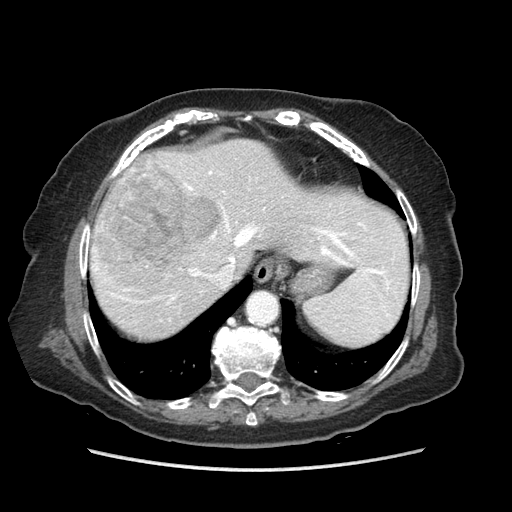
Contrast-enhanced abdominal CT (liver protocol), one axial slice; slice 67 of 89 in the series (ordered by position); soft-tissue window (W 400 / L 40 HU); 512 × 512 image matrix, field of view 360 × 360 mm. From the clinical record (not read from this slice): diagnosis: hepatocellular carcinoma (patient treated with transarterial chemoembolisation; whether this scan precedes or follows treatment is not stated here); TNM stage (as recorded): Stage-IIIA; Child-Pugh class: A; tumour nodularity: multinodular.
Outlined on this slice (semi-automatic segmentation, software-assisted and operator-edited):
- abdominal aorta: box from (x=248, y=293) to (x=277, y=324) px
- liver parenchyma outside the tumour (the mass and vessels are separate outlines, so this box may not span the whole liver): (x=90, y=138)–(x=406, y=338)
- mass: (x=95, y=156)–(x=218, y=286)
- liver vessels: (x=93, y=171)–(x=366, y=304)